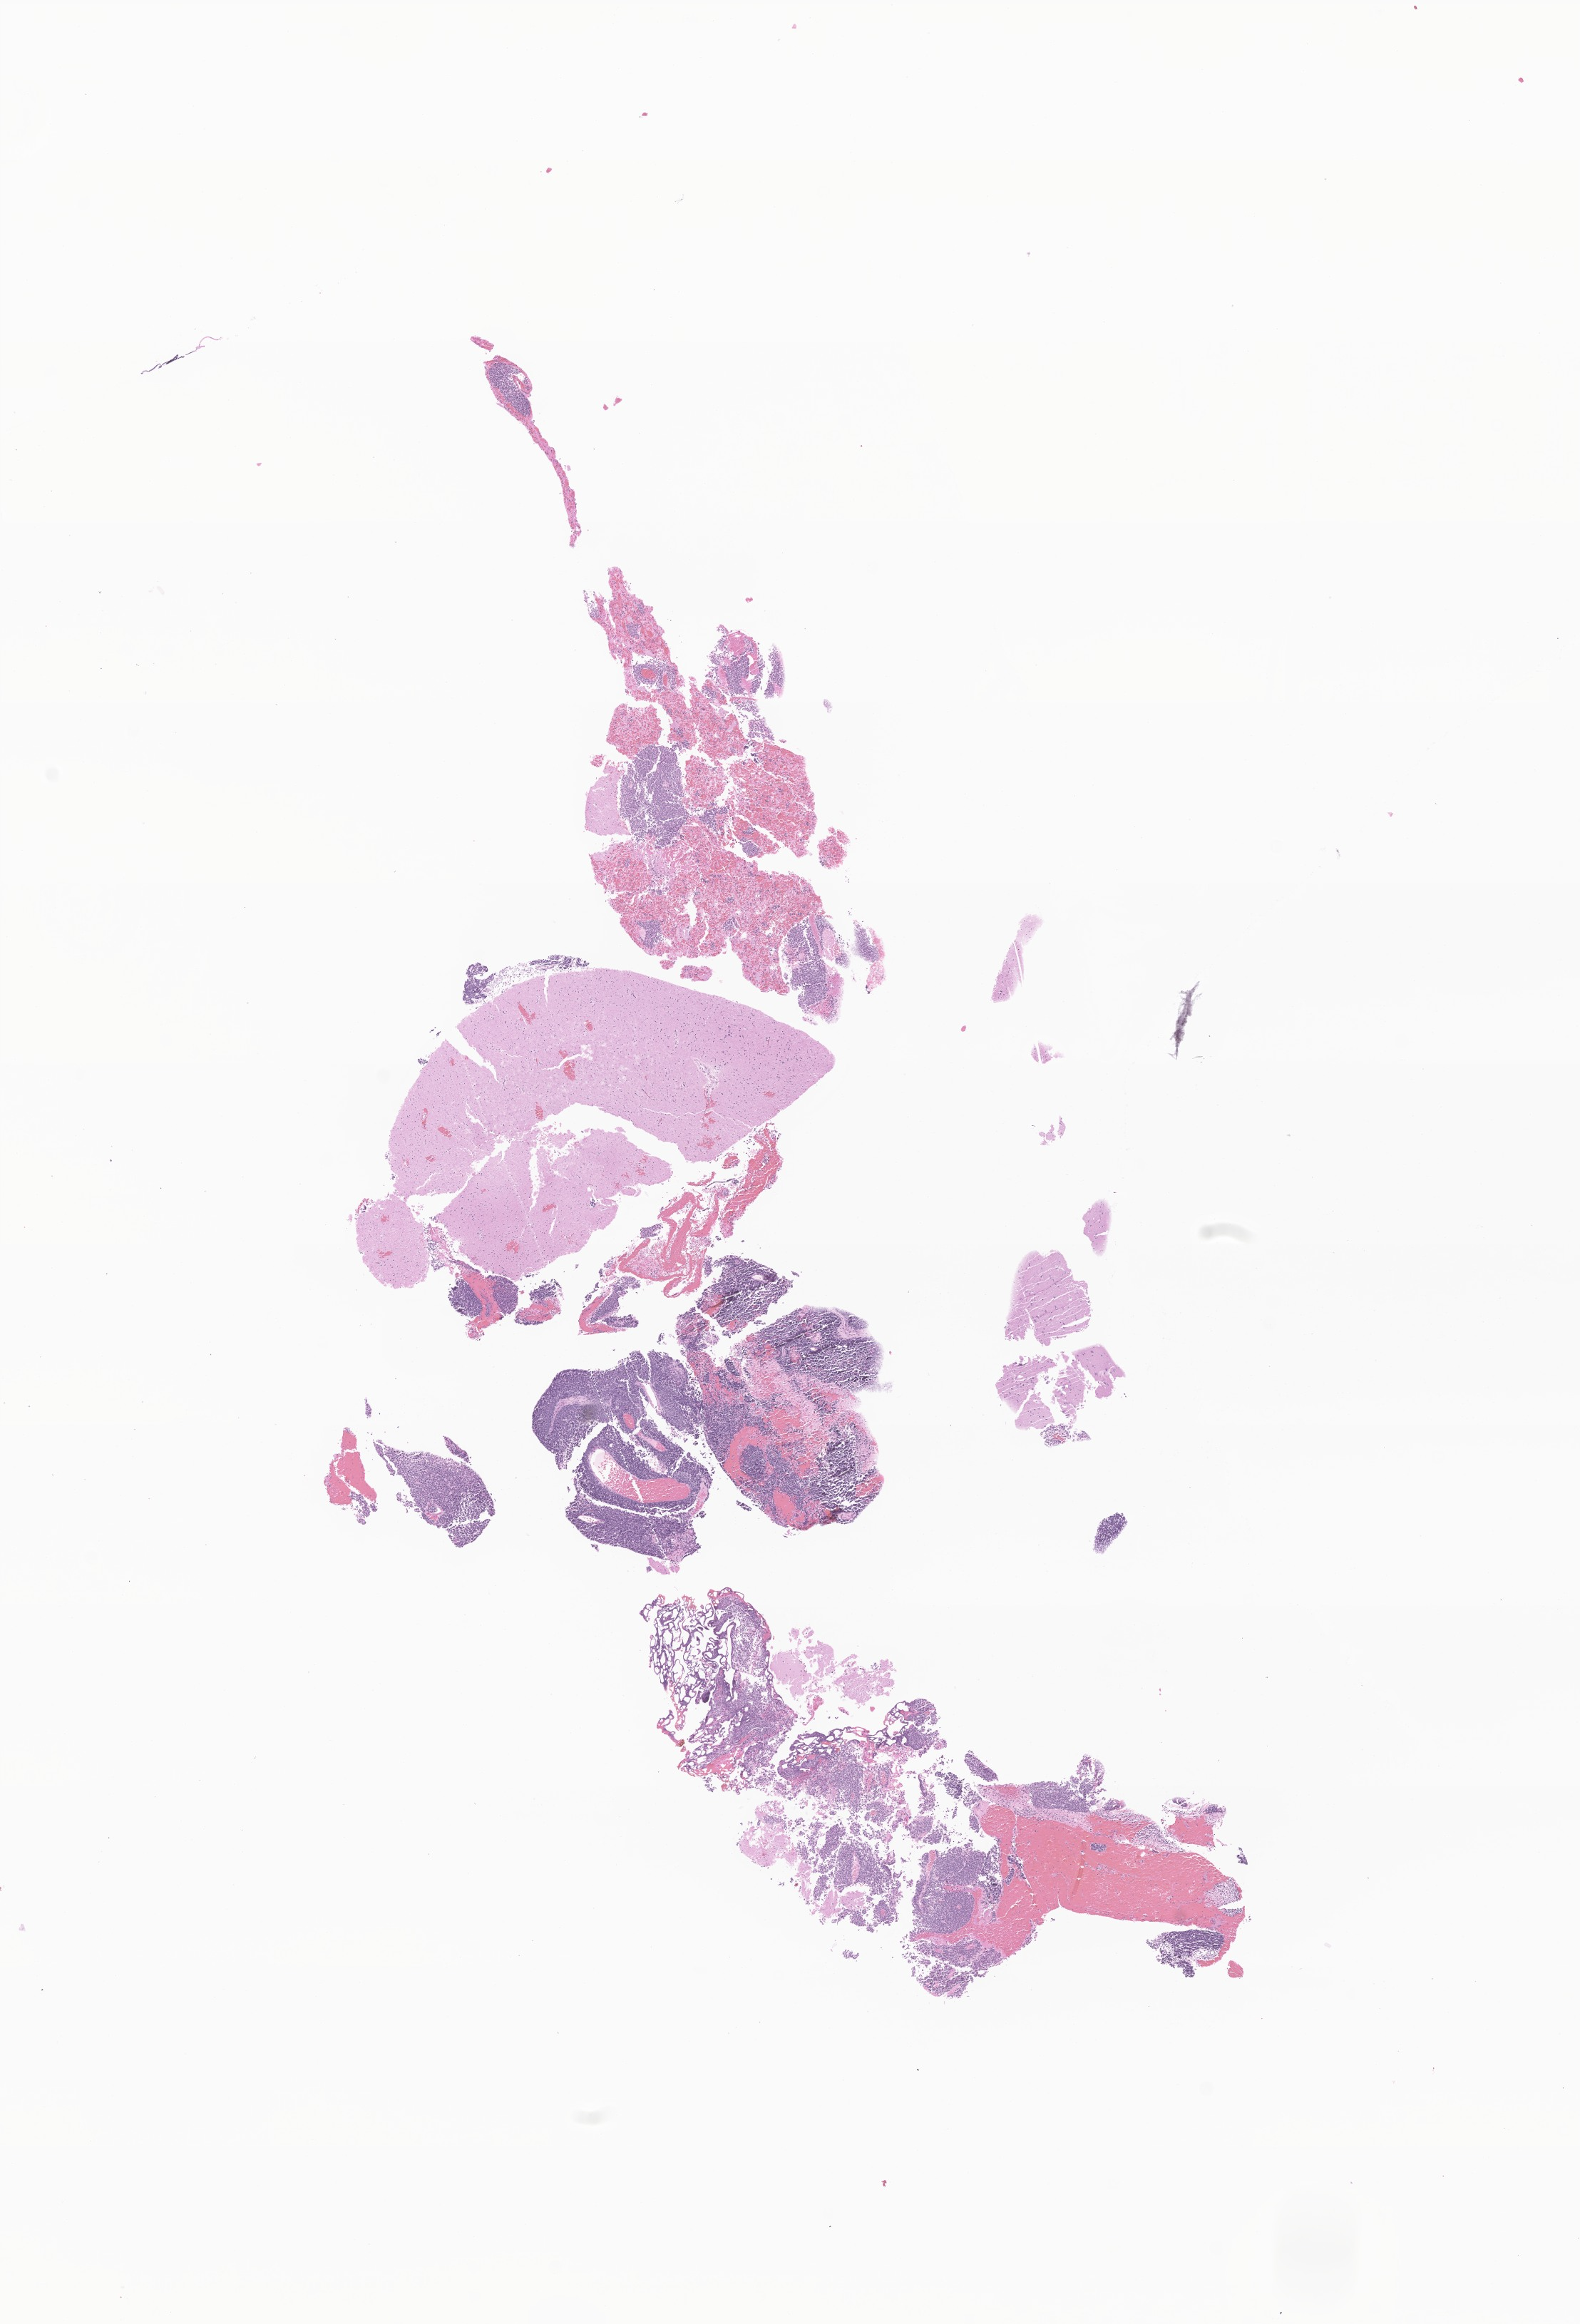
Haematoxylin and eosin whole-slide image of tumor tissue from the brain — whole scanned area (about 9.3 x 13.7 mm) shown as a low-resolution overview; formalin-fixed paraffin-embedded section. Female patient, age 57 months (4 years 9 months).
Diagnosis (ICD-O-3 morphology term): Pineoblastoma.